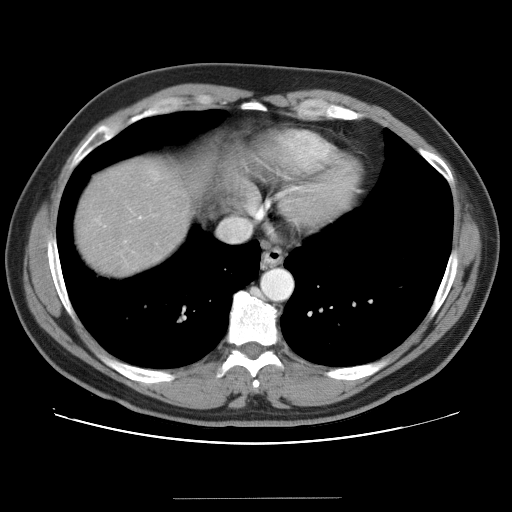
Contrast-enhanced abdominal CT (liver protocol), one axial slice. Position 35 of 40 along the scan axis. Reconstruction kernel STANDARD. 120 kVp. Soft-tissue window (W 400 / L 40 HU). 512 × 512 image matrix, field of view 380 × 380 mm. From the clinical record (not read from this slice): diagnosis: hepatocellular carcinoma (patient treated with transarterial chemoembolisation; whether this scan precedes or follows treatment is not stated here); TNM stage (as recorded): Stage-IVA; Child-Pugh class: B.
Outlined on this slice (semi-automatically segmented with operator editing):
- liver parenchyma outside the tumour (the mass and vessels are separate outlines, so this box may not span the whole liver): bounding box [x1, y1, x2, y2] px = [76, 160, 190, 274]